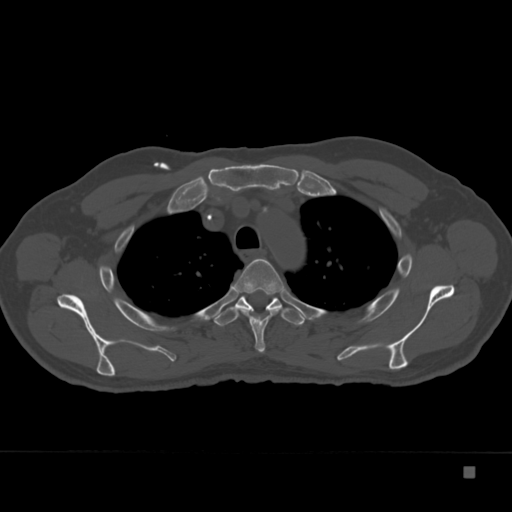
CT including the spine, one axial slice; slice 279 of 332 in the series (ordered by position); reconstruction kernel Br40s; bone window (W 1800 / L 400 HU); 512 × 512 image matrix, field of view 389 × 389 mm. Male patient, age 72 years. From the clinical record (not read from this slice): primary cancer: skeletal.
Outlined on this slice (semi-automatic segmentation, software-assisted and operator-edited):
- T3 vertebra: bounding box (x1, y1, x2, y2) in pixels: (232, 258, 285, 353)
- T4 vertebra: (214, 296, 306, 327)